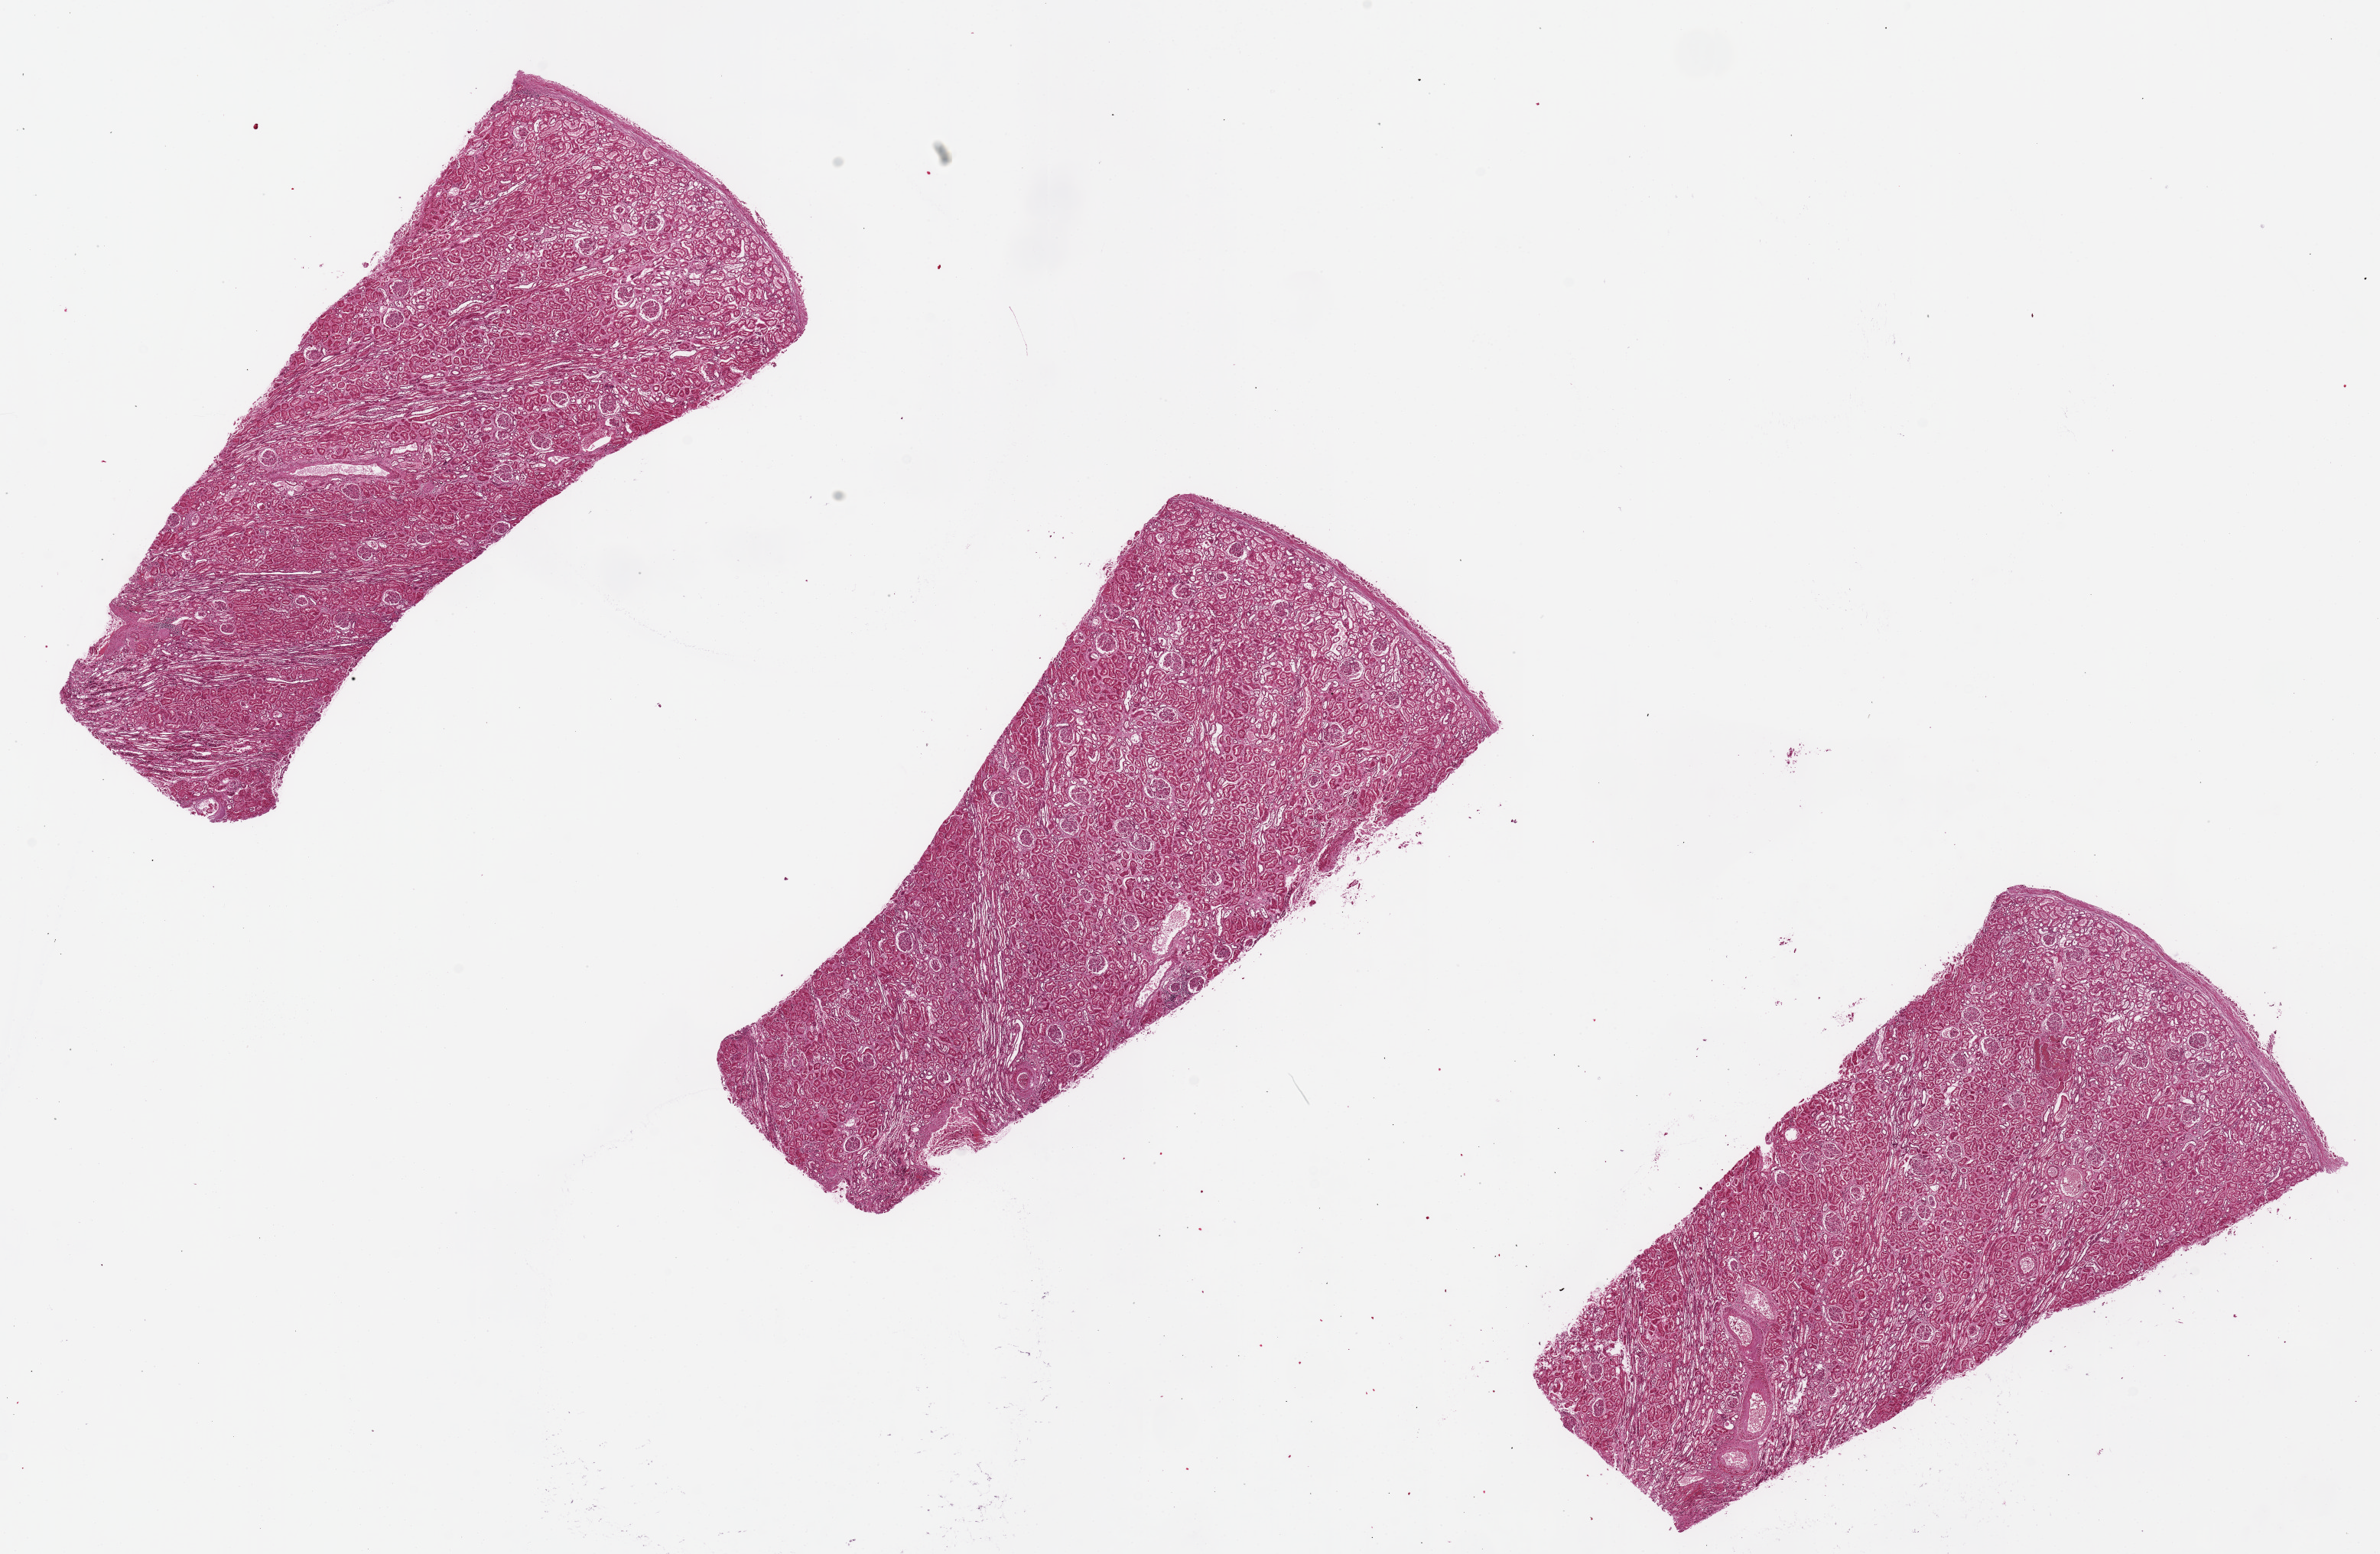
Whole-slide image, H&E stain — whole scanned area (about 24.6 x 16.1 mm) shown as a low-resolution overview, PAXgene-fixed paraffin-embedded (PFPE) section, section of renal cortex (target tissue), donor tissue sample. Female donor.
- reviewer comment on this tissue sample: 3 pieces 8x4 Cortex